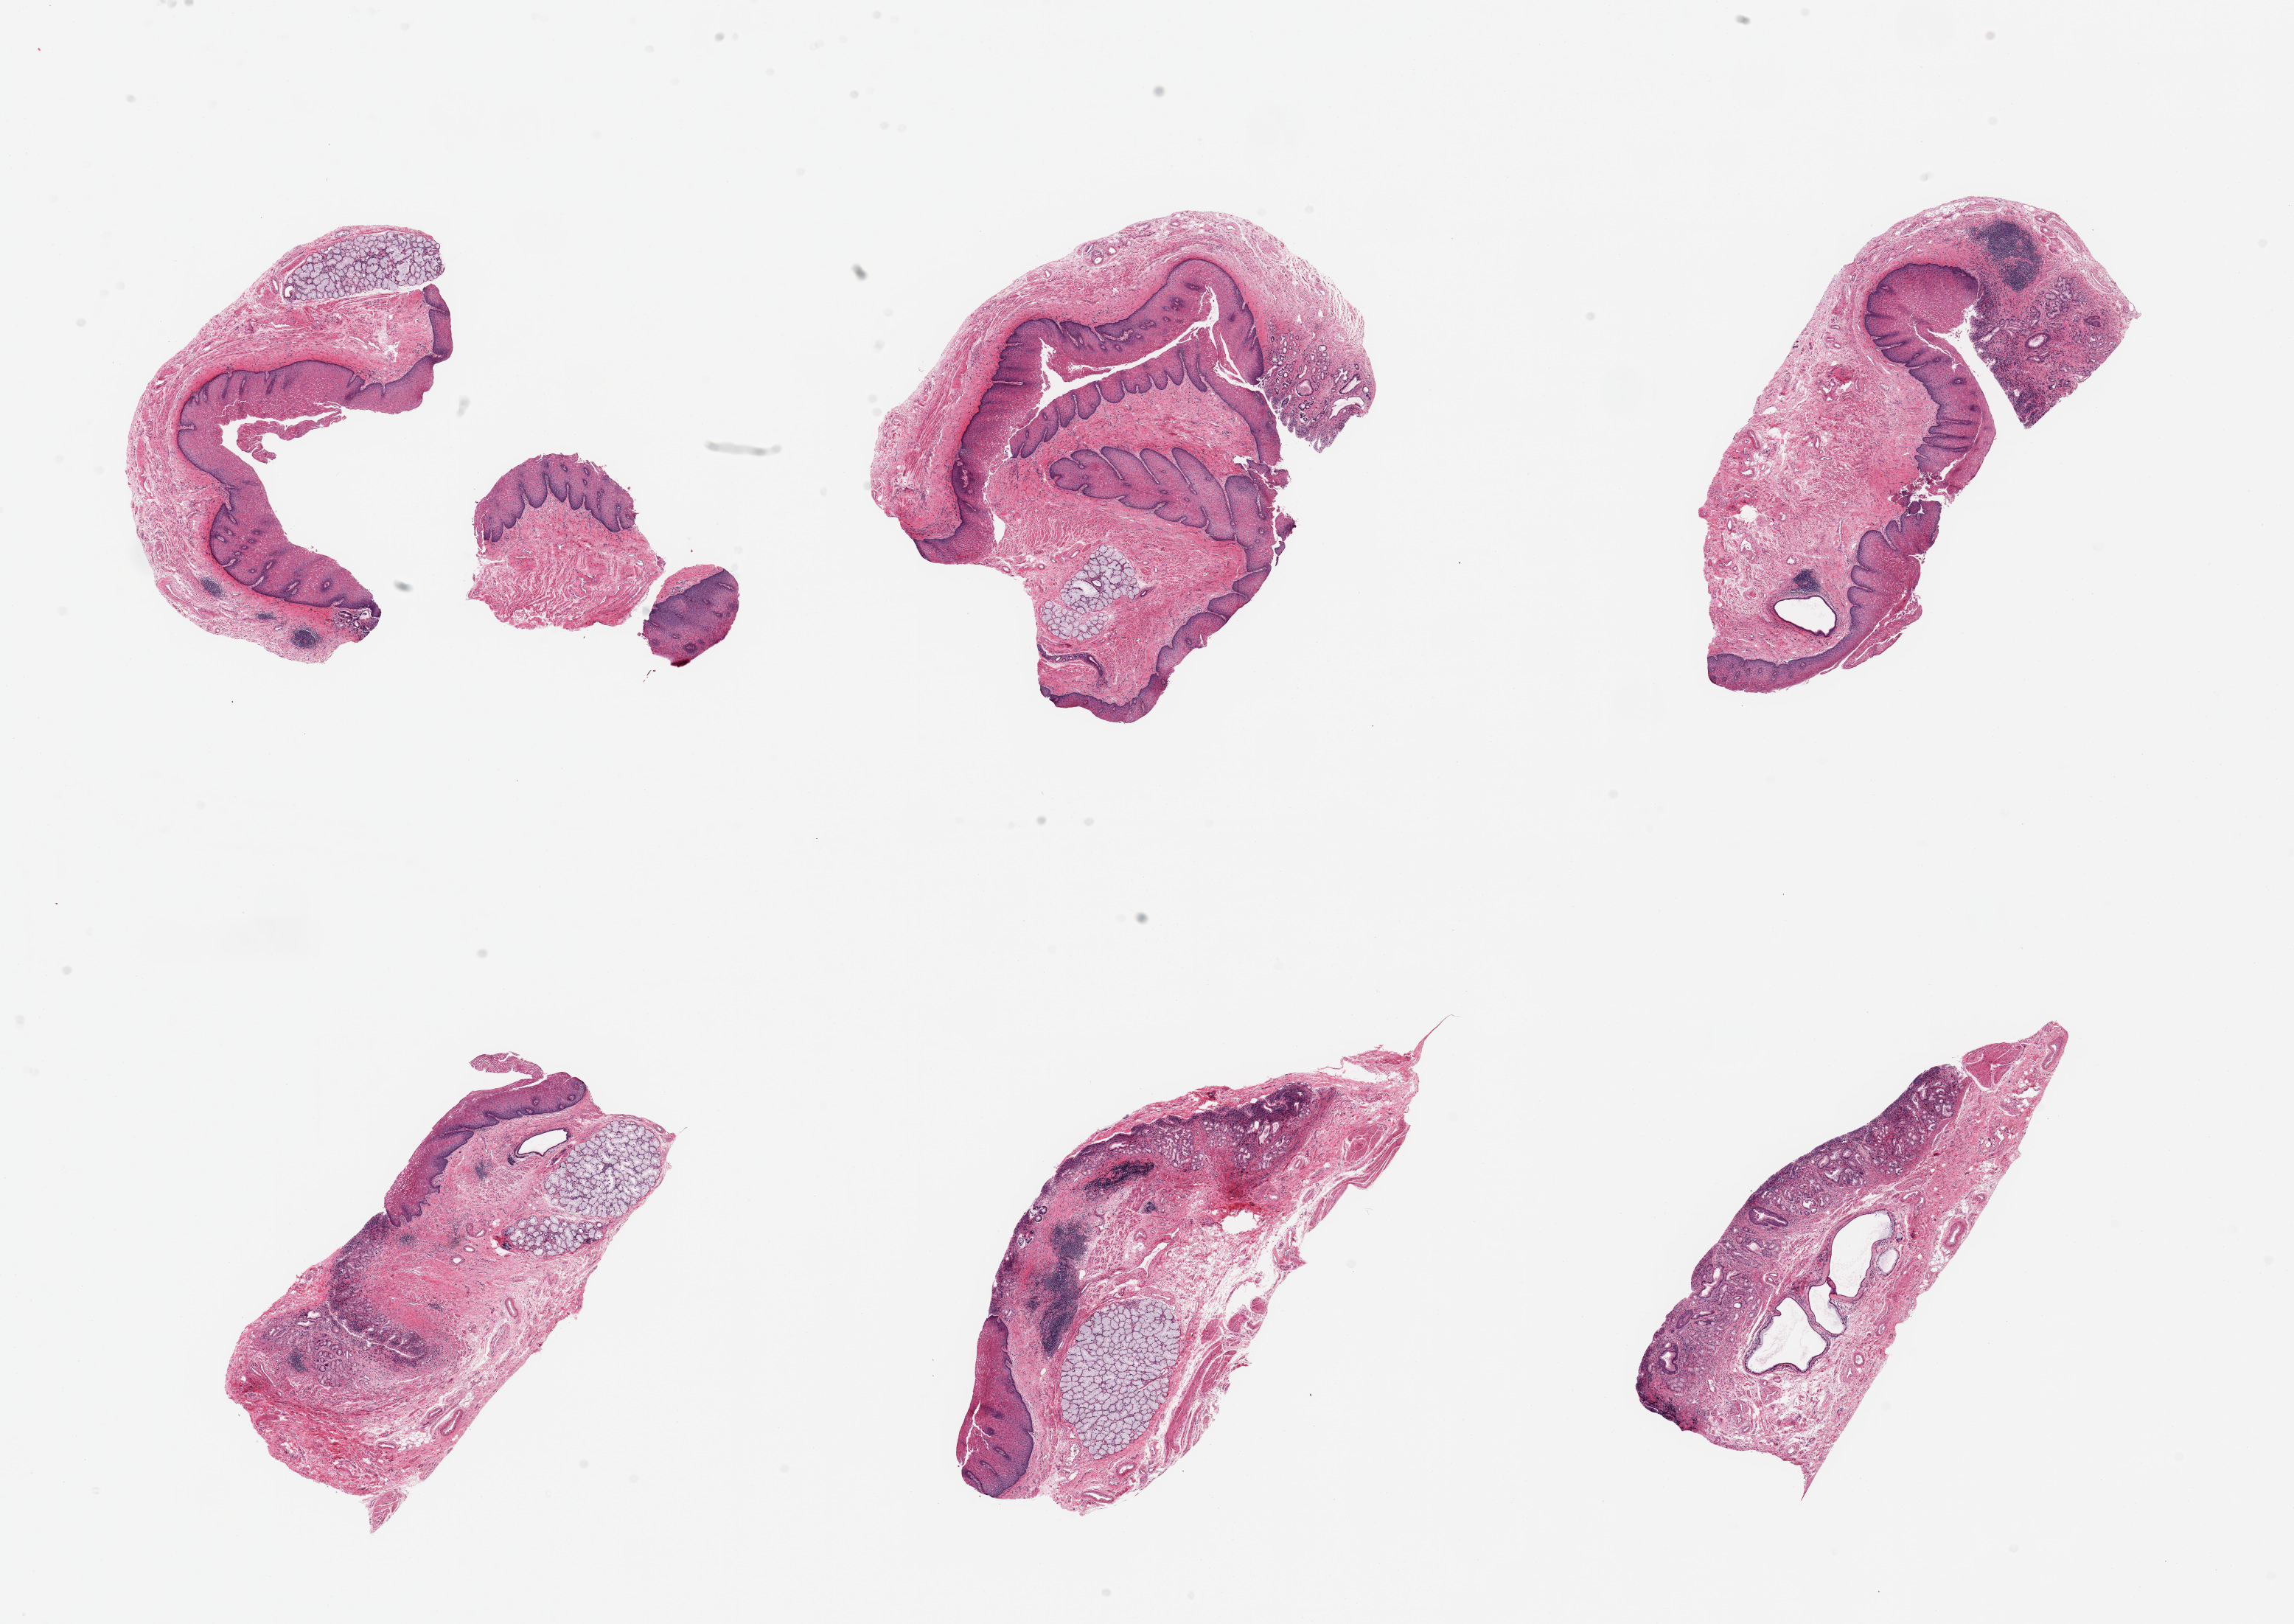
Digitized haematoxylin and eosin-stained section, low-resolution overview of the scanned area, about 24.6 x 17.4 mm (slide scanned at 20x), PAXgene-fixed paraffin-embedded (PFPE) section, sampled site (target tissue): gastroesophageal junction, tissue donor sample. Donor sex: male.
• review note (as recorded): 6 pieces, ~50% squamous mucosa, rest is stroma/mucus glands. <10% target muscularis present